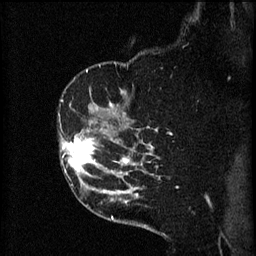
Breast MRI (dynamic contrast-enhanced), one sagittal slice. Slice 43 of 60 in the series (ordered by position). 3 images stored at this slice position (order not interpretable as contrast timing). 1.5 T. TE 4.2 ms, TR 8.2 ms. 2 mm slice thickness. 256 × 256 image matrix, field of view 180 × 180 mm. Female patient, age 49 years.
Outlined on this slice (semi-automatic segmentation, software-assisted and operator-edited):
- analysis volume of interest (the breast-tissue region the enhancement analysis was run in; not a lesion): bounding box (x1, y1, x2, y2) in pixels: (60, 128, 105, 177)
- tumour enhancement mask (voxels above the 70 % enhancement threshold inside the analysis volume of interest): (60, 134, 99, 177)